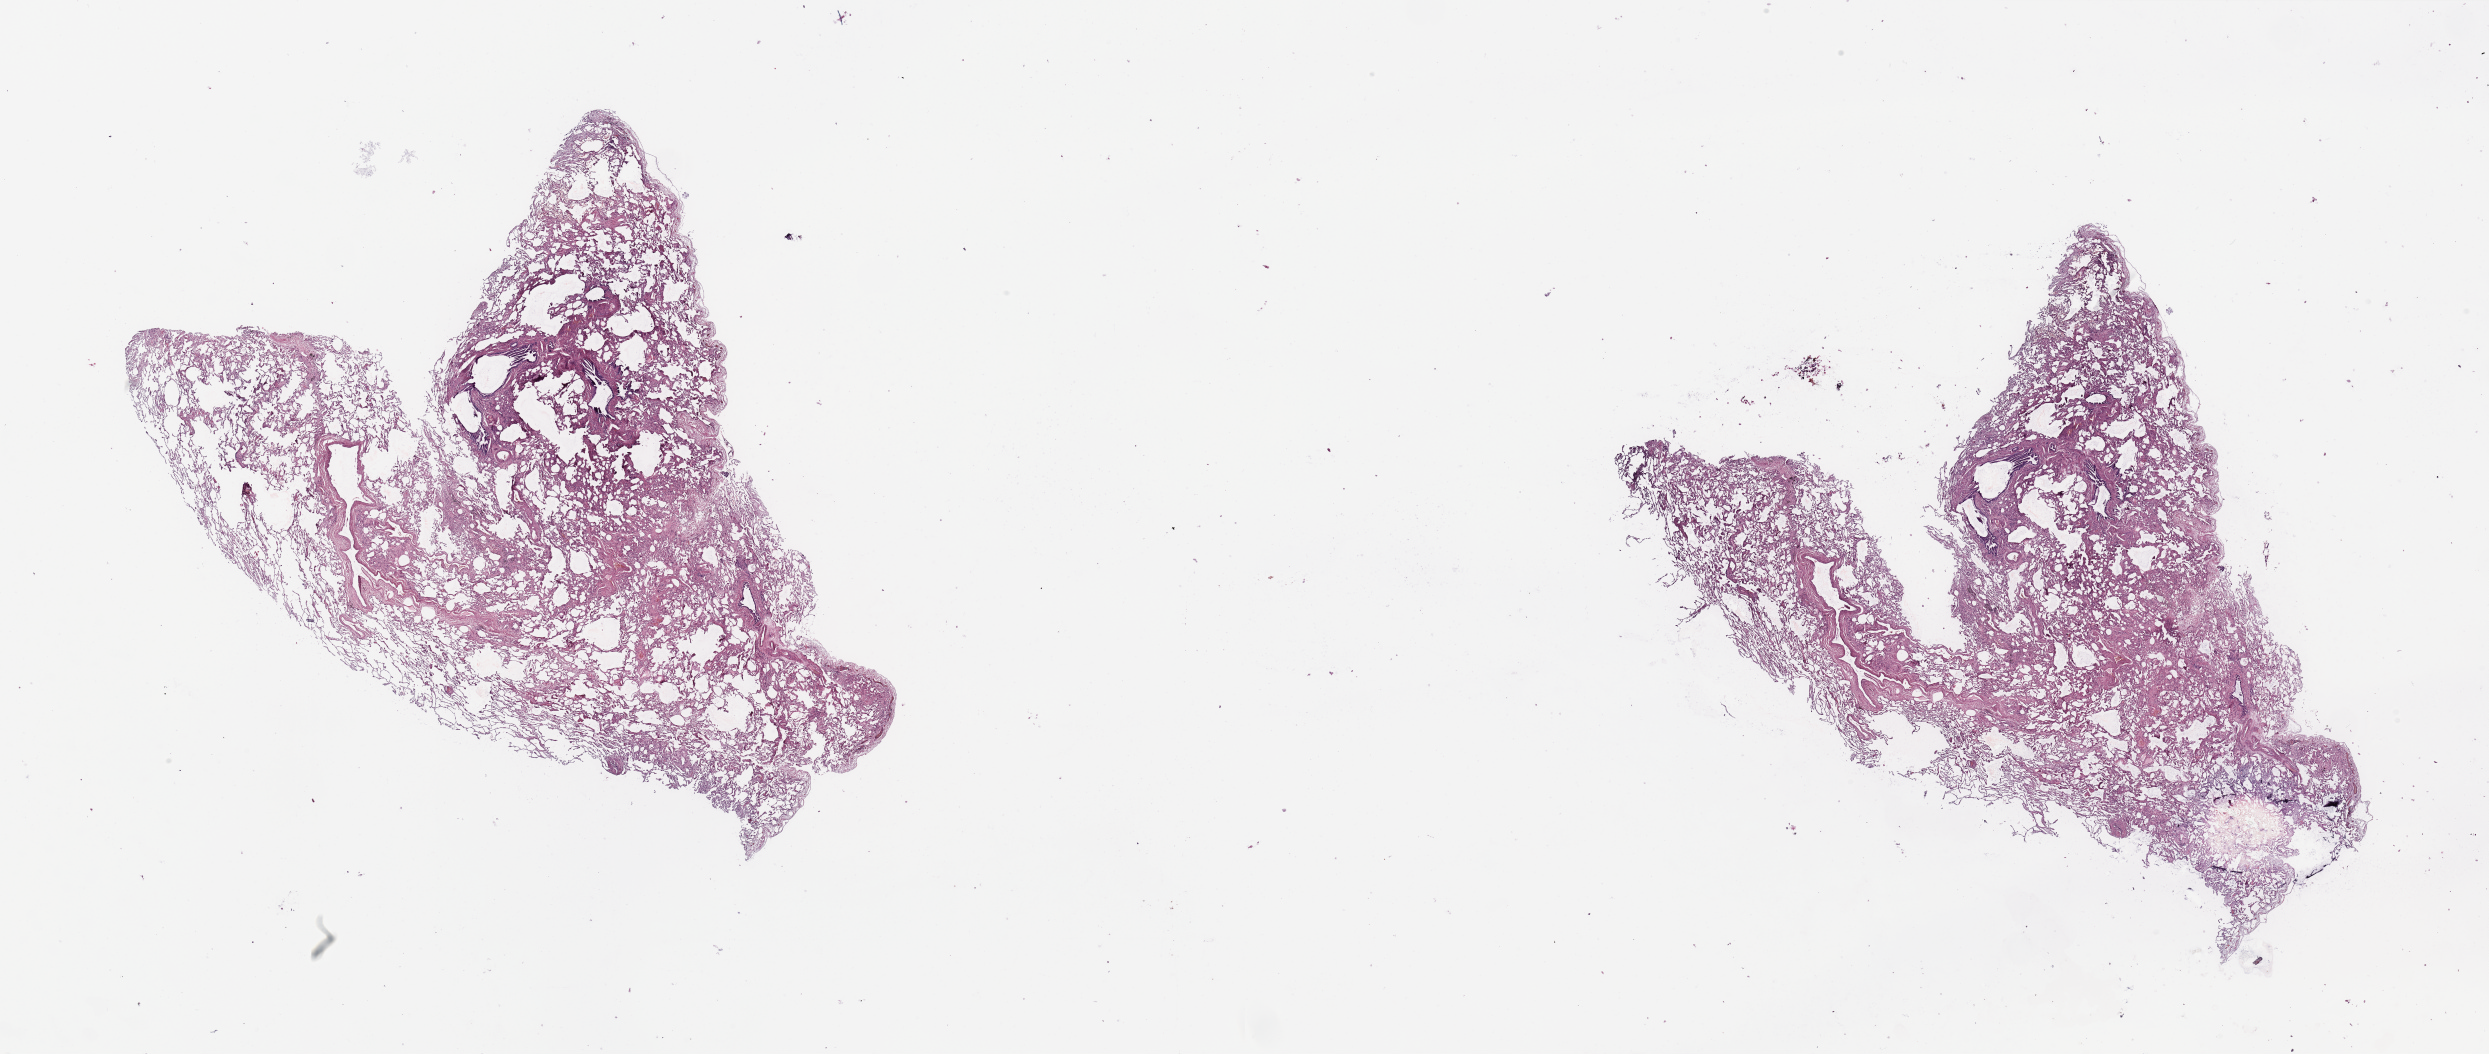
Whole-slide histology image, Hematoxylin and eosin (H&E) stained — shown as a low-resolution overview of the whole scanned area (about 39.4 x 16.7 mm, from a 20x scan), lung, normal (non-tumour) tissue. Female, 70 y/o.
This section: normal (non-tumour) tissue from the same patient. Patient diagnosis: Squamous cell carcinoma, NOS.